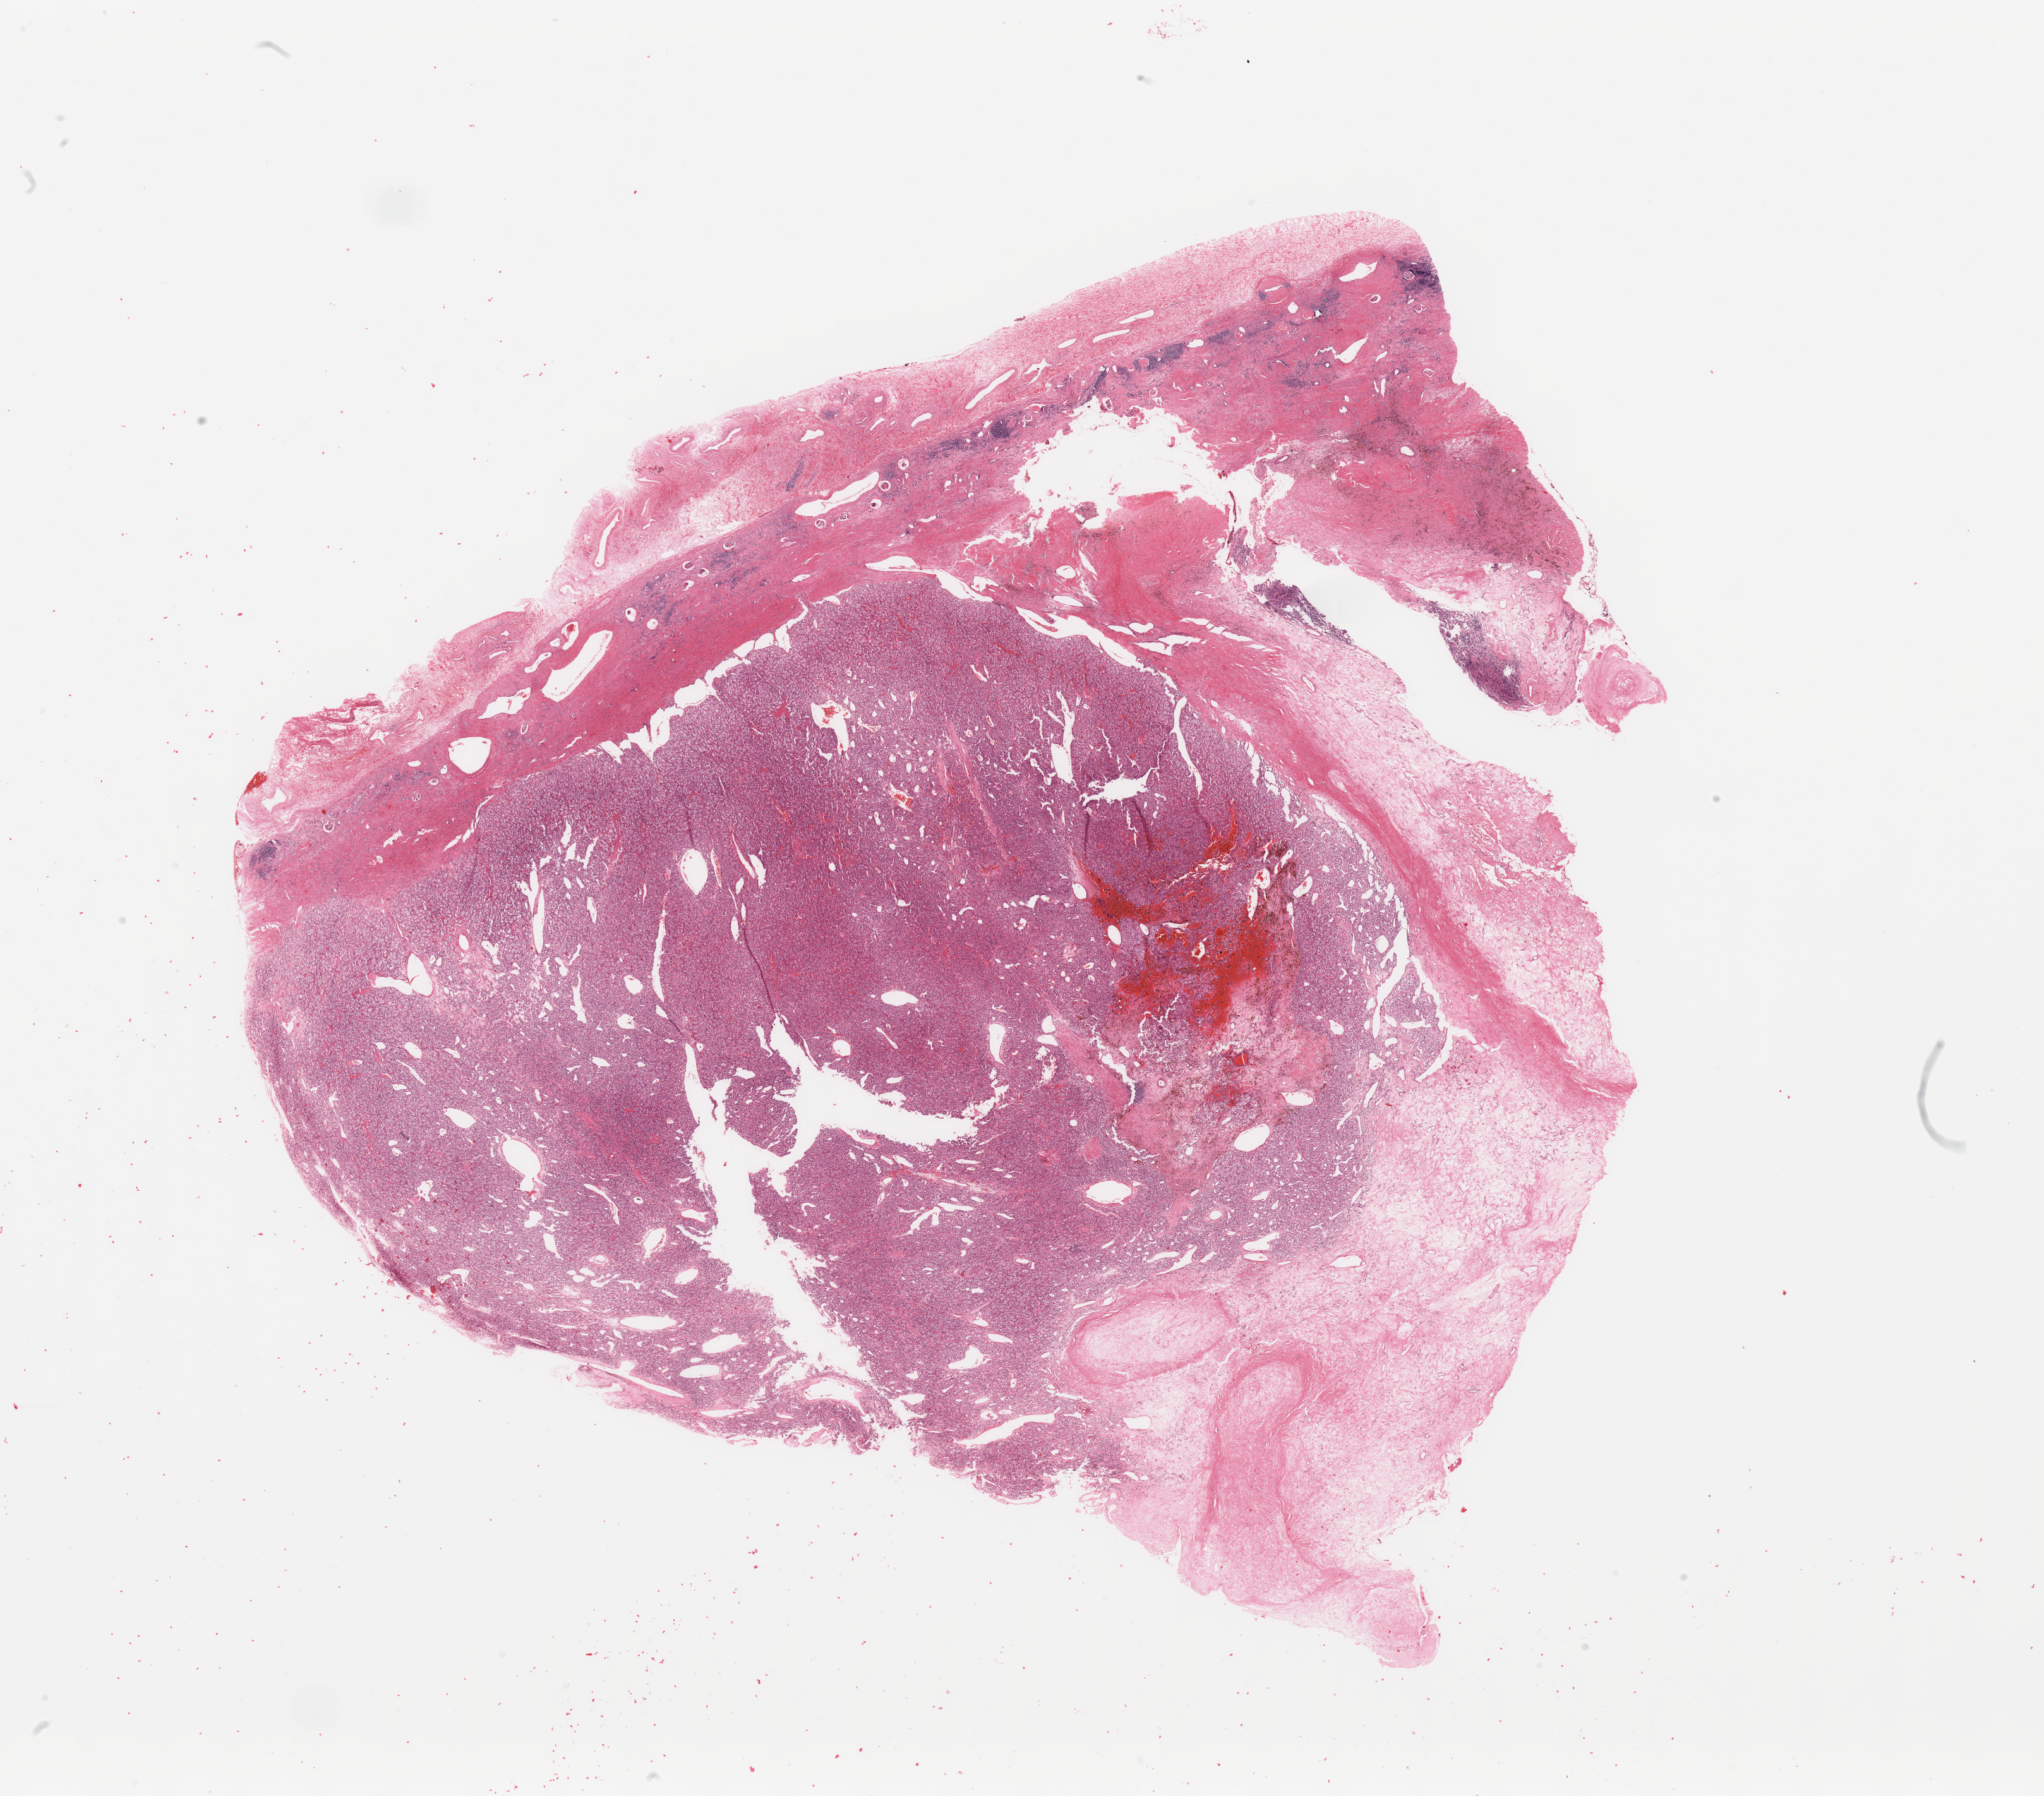
H&E-stained whole-slide image, low-resolution overview of the scanned area, about 25.6 x 22.5 mm (slide scanned at 20x), tumour tissue sample, sampled site: kidney. 57-year-old female patient.
Histologic diagnosis: Renal cell carcinoma, NOS.